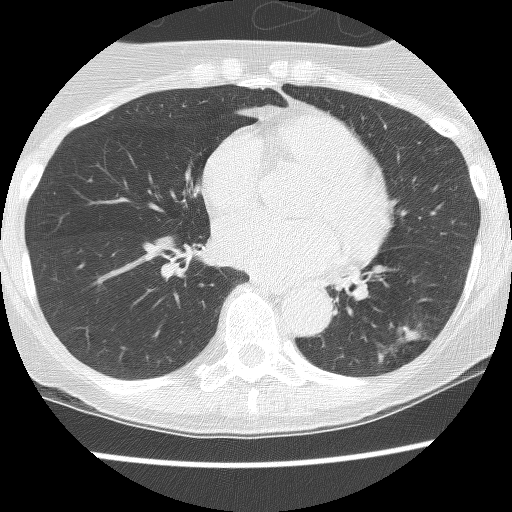
Low-dose screening chest CT, axial slice, third screening round (two years after baseline), lung window (W 1500 / L -600 HU), 512 × 512 image matrix, field of view 290 × 290 mm. Female, age 61 years at enrolment. Current smoker at enrolment.
Expert reader's lesion annotation, bounding box <328,288,453,392> (left, top, right, bottom; pixels). The screening reader recorded 2 non-calcified nodules or masses ≥4 mm on this exam; which of them this box marks is not recorded. Participant outcome: lung cancer diagnosed 166 days after this screen — non-small cell carcinoma, left lower lobe, poorly differentiated (G3), stage IB (AJCC 6th edition), 100 mm at pathology.